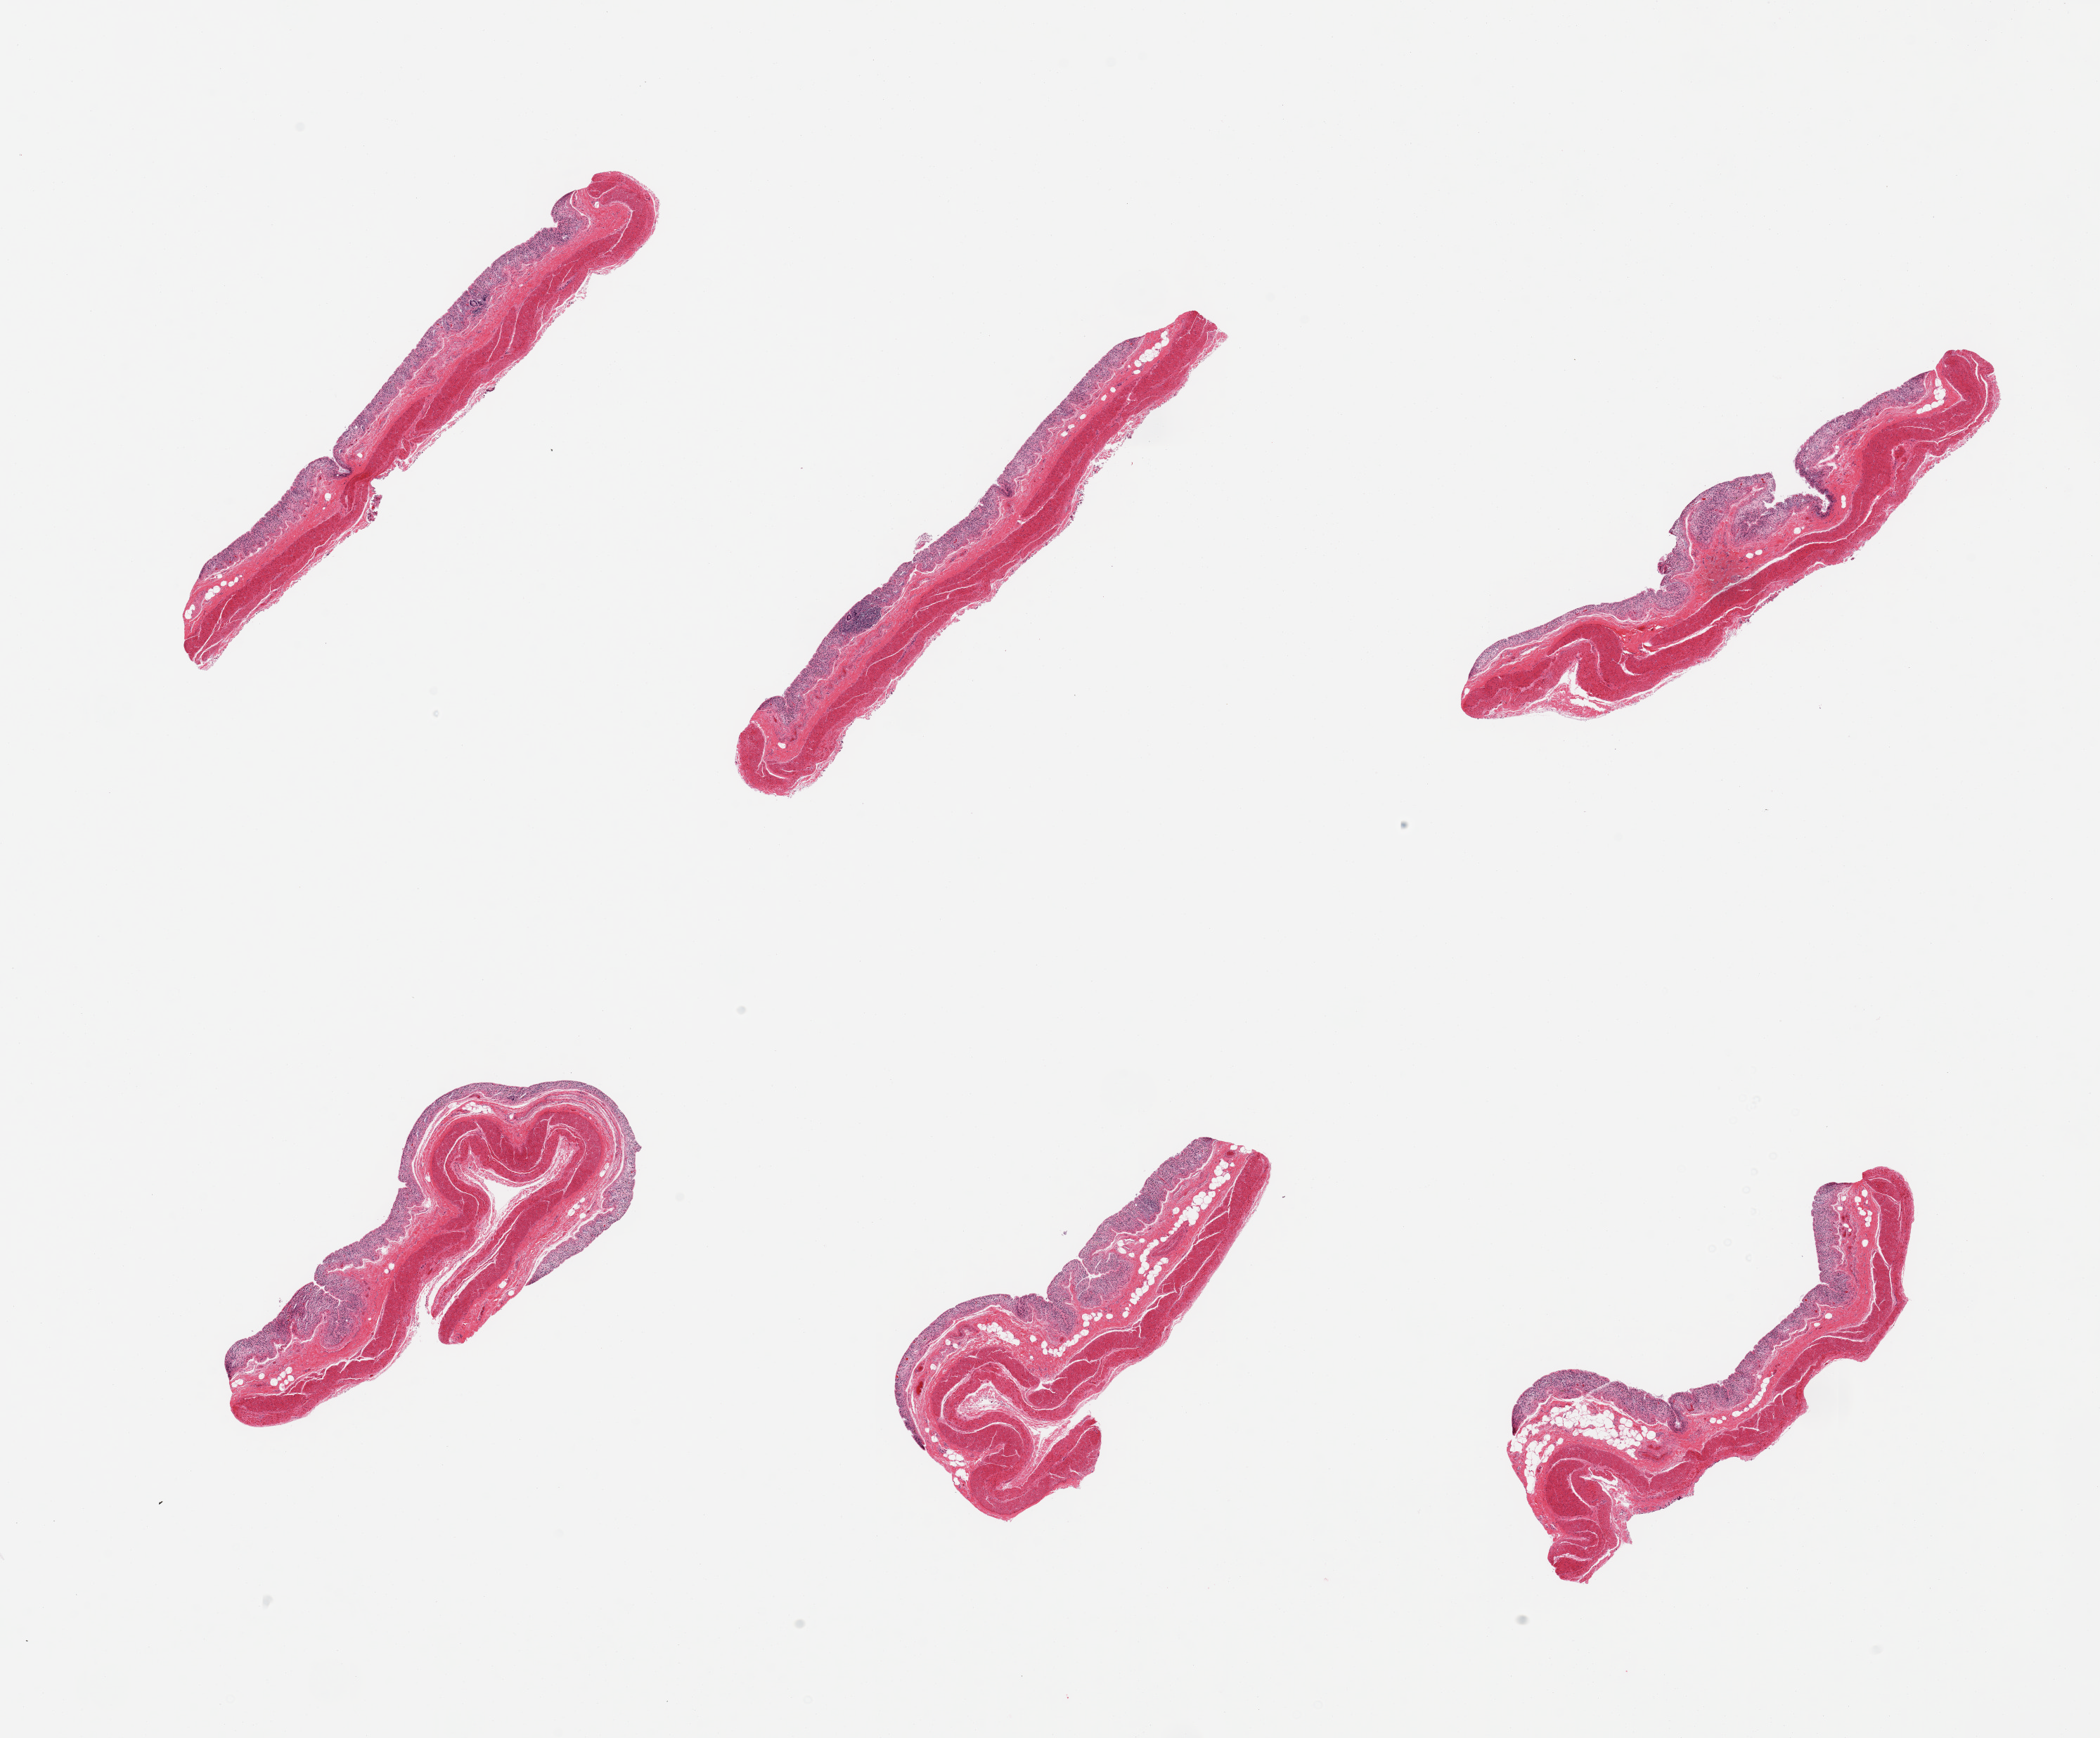
Whole-slide image, hematoxylin and eosin (H&E) stain — whole scanned area (about 23.6 x 19.6 mm) shown as a low-resolution overview; PAXgene-fixed paraffin-embedded (PFPE) section; section of transverse colon (target tissue); tissue donor sample. Male donor.
Review note (as recorded): 6 pieces; mucosa totally autolyzed, muscle preserved.